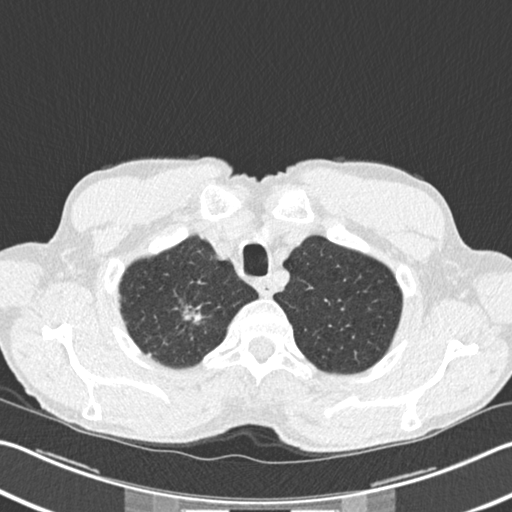
Low-dose screening chest CT, one axial slice. Slice 195 of 220 in the series (ordered by position). Reconstruction kernel B30f. 120 kVp. Lung window (W 1500 / L -600 HU). 2 mm slice thickness. 512 × 512 image matrix.
Outlined on this slice (outlined manually by an expert reader):
- lesion 1 (tumor, upper lobe of right lung): bounding box [x1, y1, x2, y2] px = [184, 307, 203, 324]